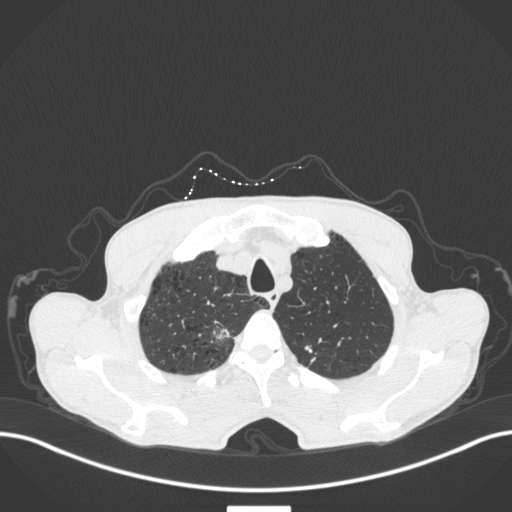
Chest CT, one axial slice. Slice 369 of 445 in the series (ordered by position). Reconstruction kernel B31f. Lung window (W 1500 / L -600 HU). 1 mm slice thickness. 512 × 512 image matrix. Male patient, age 70 years. From the clinical record (not read from this slice): clinical TNM (as recorded): T1a N0 M0.
Structures marked on this image (rectangle marked by the reading radiologist):
- lung tumour (recorded histology: adenocarcinoma): box from (x=208, y=317) to (x=232, y=346) px